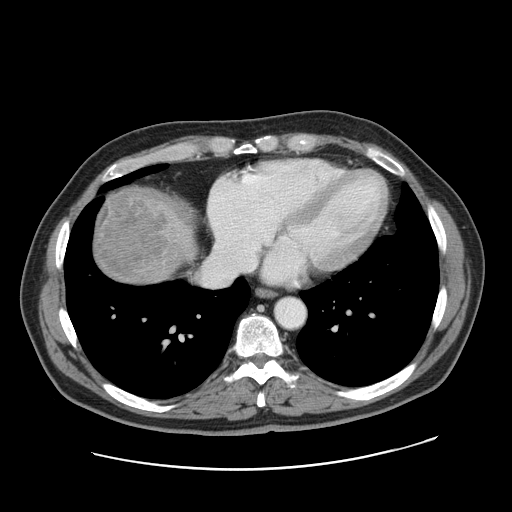
Contrast-enhanced abdominal CT, one axial slice. Position 156 of 178 along the scan axis. Intravenous contrast given. Soft-tissue window (W 400 / L 40 HU). 2.5 mm slice thickness. 512 × 512 image matrix, field of view 403 × 403 mm. Male patient, age 63 years. Case-level facts recorded for this patient, not image findings: diagnosis: colorectal cancer liver metastases, imaged before liver resection; multiple liver metastases: yes; largest metastasis: 8 cm; chemotherapy before resection: no.
Outlined on this slice (manually delineated by an expert):
- liver: bounding box [x1, y1, x2, y2] px = [92, 188, 196, 286]
- liver metastasis: [96, 189, 164, 283]